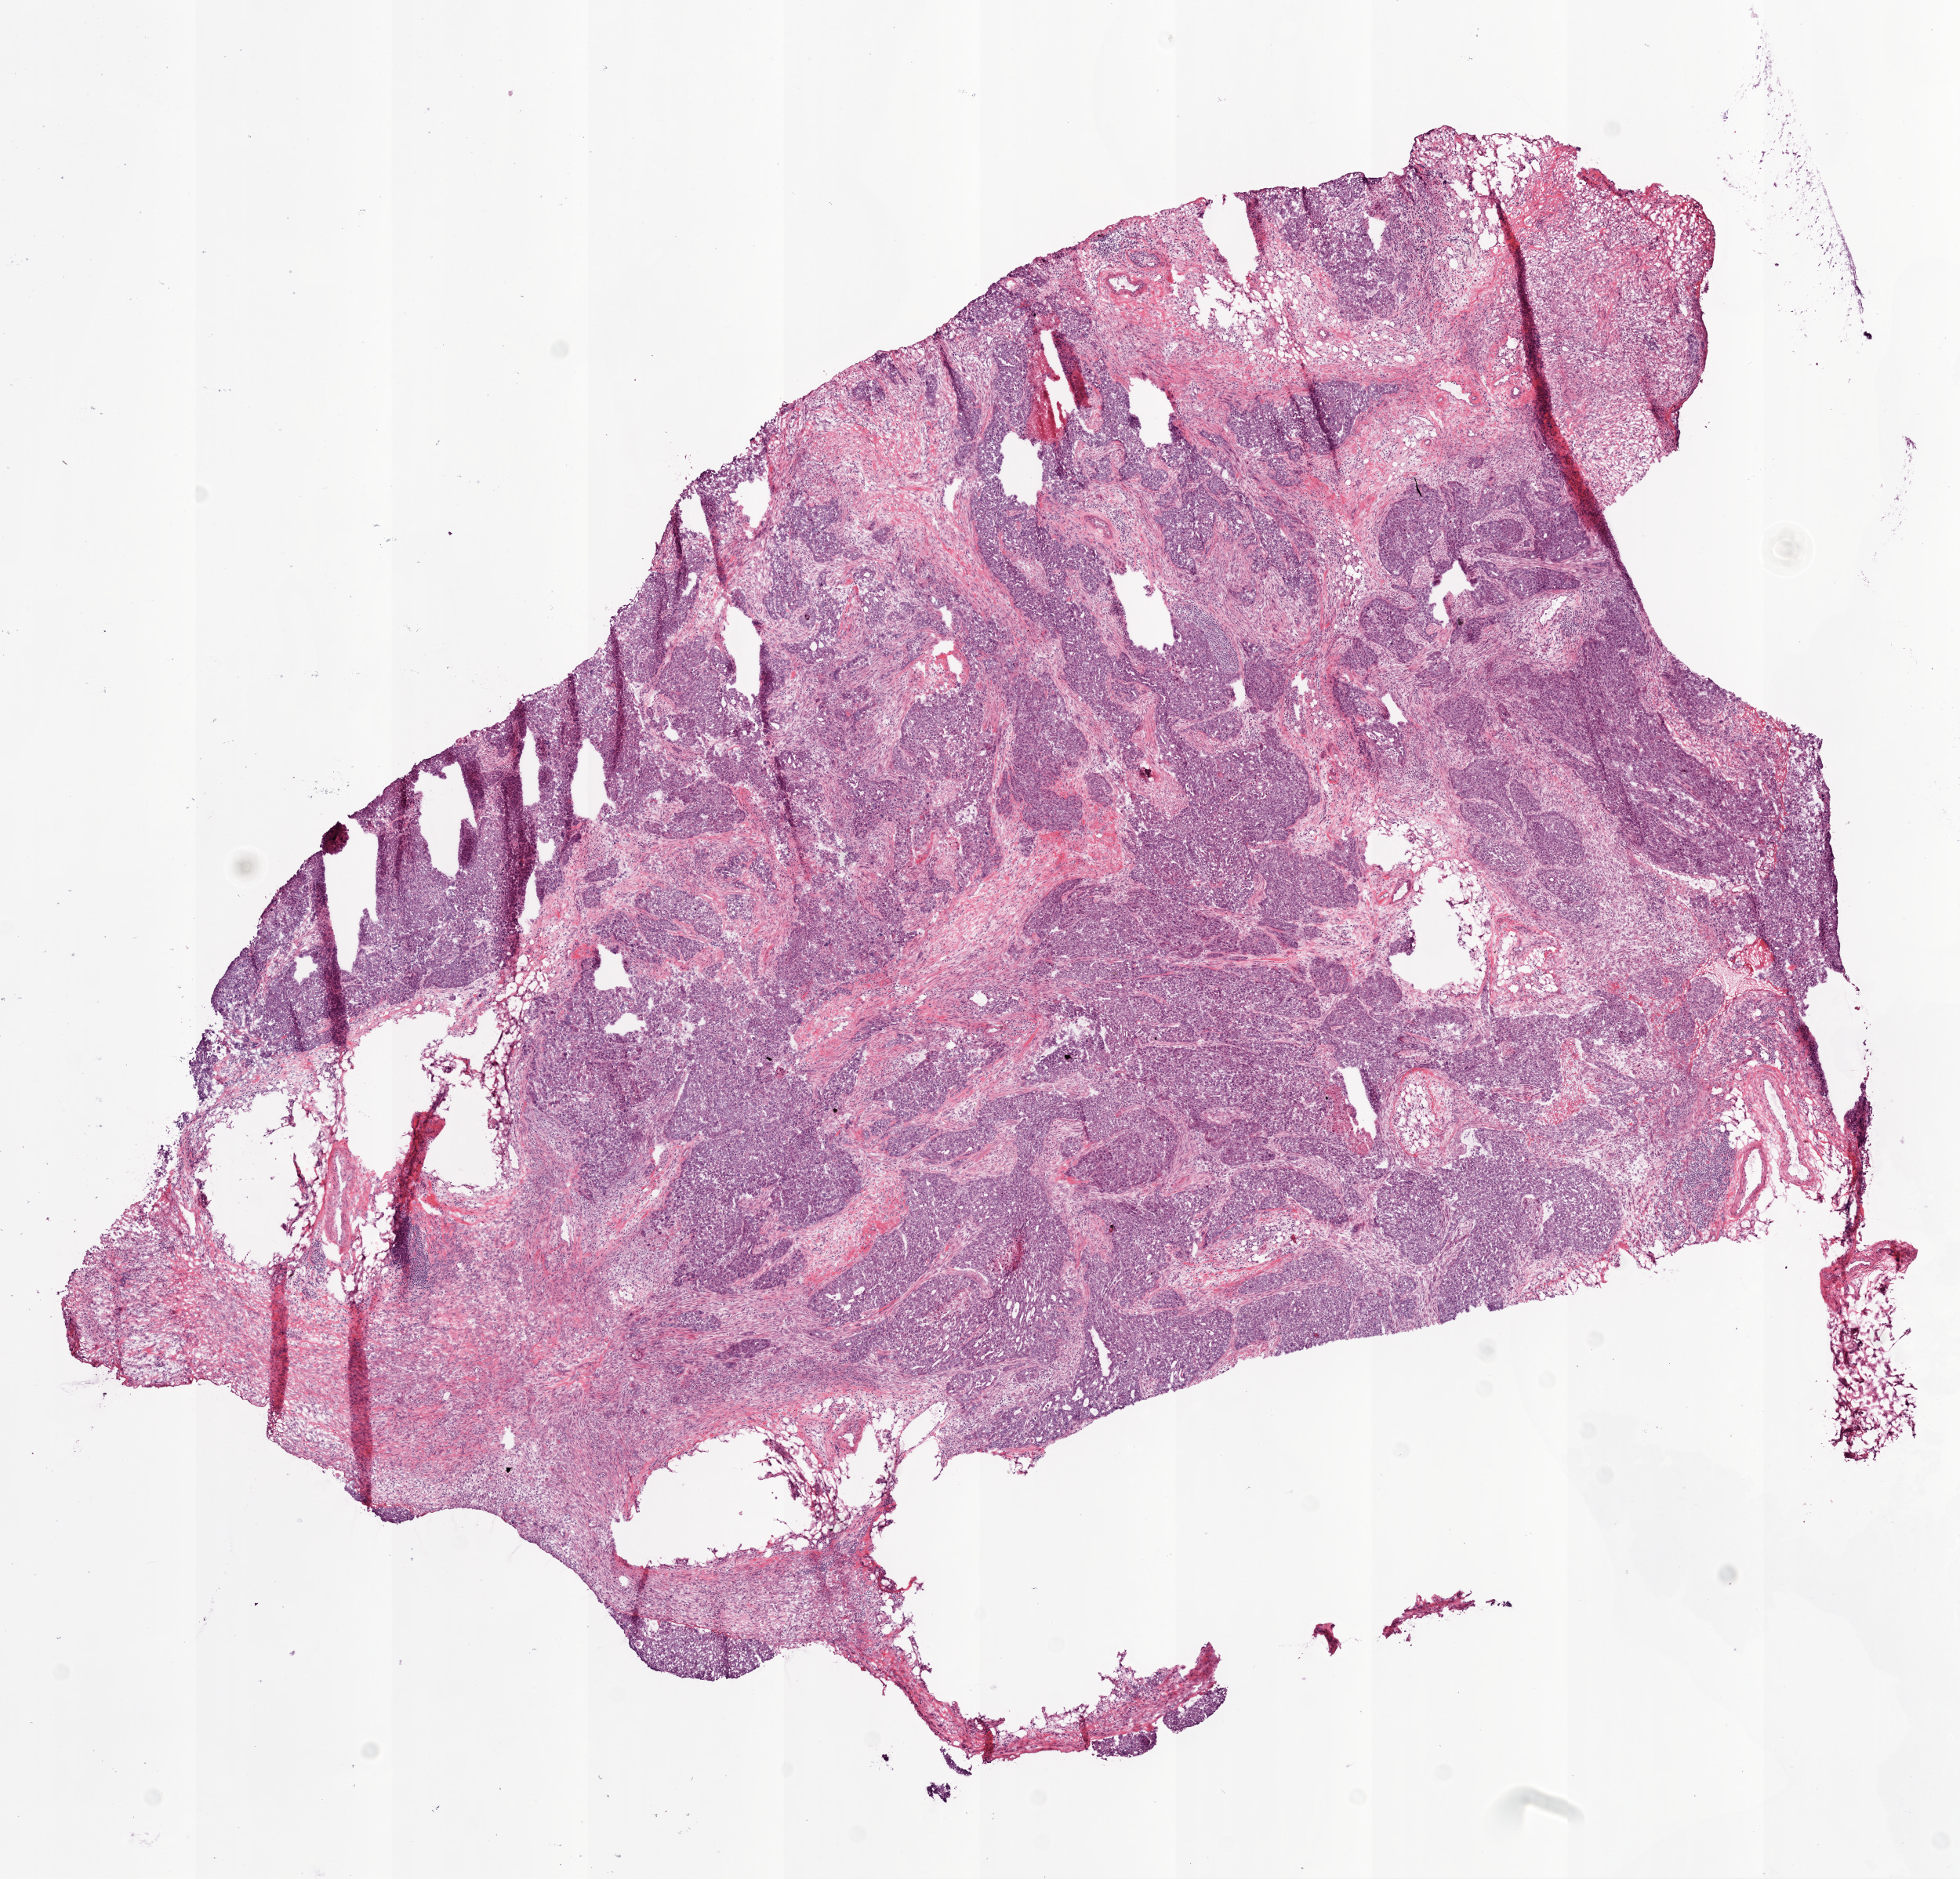
Digitized H&E-stained tissue section (whole slide) — low-resolution overview of the scanned area, about 10.0 x 9.6 mm; frozen section; primary tumour sample from the ovary. Female, age 56 years at initial diagnosis. Histologic grade: GX (grade cannot be assessed). Pathologist review of this section (percent, as recorded): tumour cells 85%, tumour nuclei 80%, normal cells 0%, stromal cells 14%, necrosis 1%. Inflammatory infiltration, as recorded: lymphocyte infiltration 5%.
- histologic diagnosis: Serous cystadenocarcinoma, NOS
- FIGO stage: IIIC